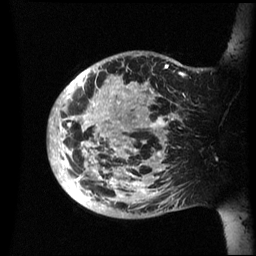
Breast MRI (dynamic contrast-enhanced), one sagittal slice; position 14 of 60 along the scan axis; dynamic contrast-enhanced series, image 2 of 3 at this slice position (ordered by acquisition); 1.5 T; TE 4.2 ms, TR 8.4 ms; 256 × 256 image matrix. Patient: female, 48 years.
Annotated regions visible in this slice (semi-automatically segmented with operator editing):
- analysis volume of interest (the breast-tissue region the enhancement analysis was run in; not a lesion): bounding box (x1, y1, x2, y2) in pixels: (48, 51, 202, 219)
- tumour enhancement mask (voxels above the 70 % enhancement threshold inside the analysis volume of interest): (49, 65, 183, 203)